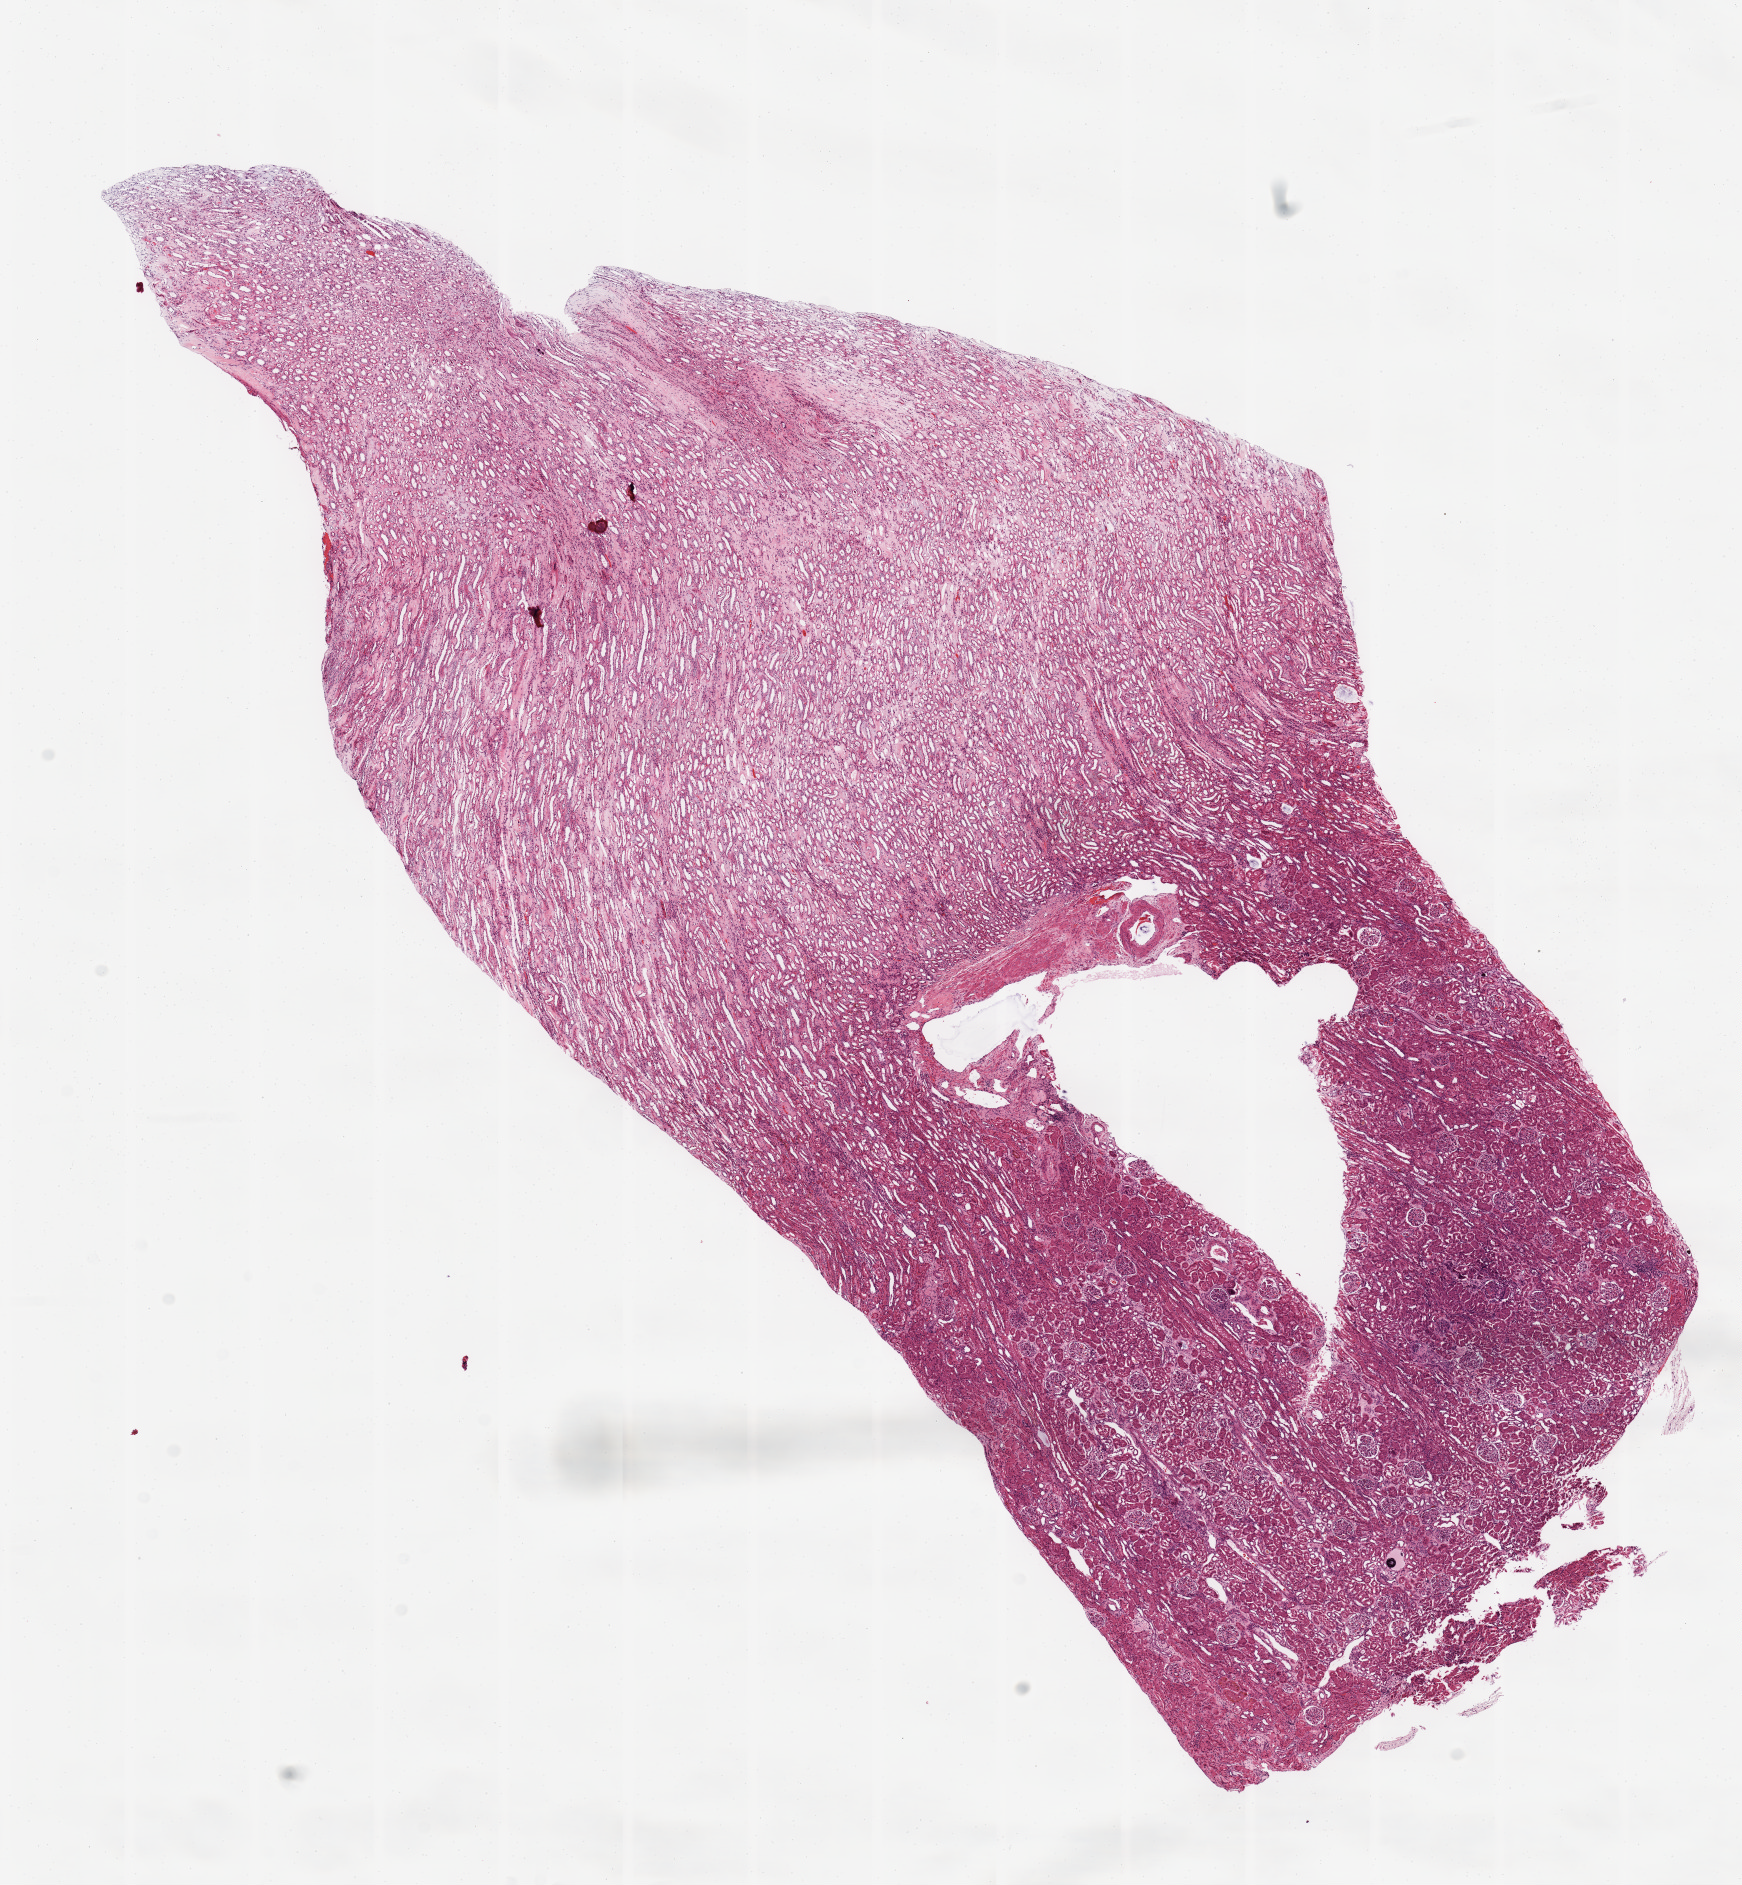
Hematoxylin and eosin (H&E) stained whole-slide image — low-resolution overview of the scanned area, about 13.8 x 14.9 mm (from a 20x scan); normal (non-tumour) tissue sample, sampled site: kidney. Male, 60 y/o.
This section: normal (non-tumour) tissue from the same patient. Patient diagnosis: Renal cell carcinoma, NOS.